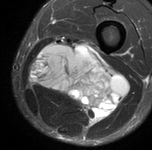
MRI of an extremity soft-tissue mass, one axial slice. Position 37 of 90 along the scan axis. STIR. MR volume resampled by the dataset authors to the PET/CT grid (not the native acquisition matrix). 3.27 mm slice thickness. 152 × 150 image matrix. Male patient. From the clinical record (not read from this slice): histological type: undifferentiated pleomorphic liposarcoma; grade: high; site of the primary tumour: left thigh.
Annotated regions visible in this slice (expert contour drawn on MRI and transferred to this co-registered scan by the dataset authors):
- gross tumour volume including surrounding oedema: bounding box (x1, y1, x2, y2) in pixels: (30, 37, 126, 124)
- gross tumour volume (mass): (34, 48, 124, 120)